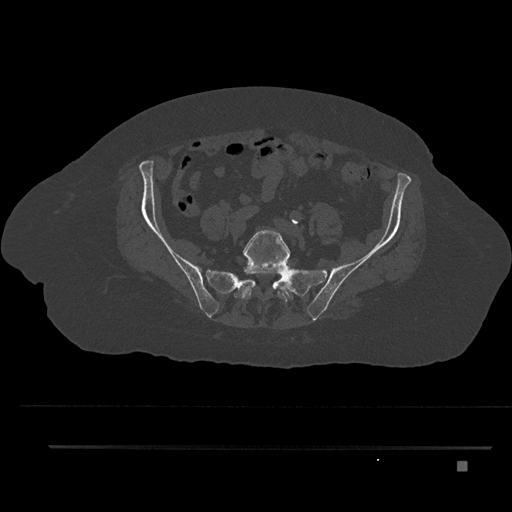
CT including the spine, one axial slice. Position 20 of 797 along the scan axis. Reconstruction kernel Br40s/3. Bone window (W 1800 / L 400 HU). 512 × 512 image matrix, field of view 437 × 437 mm. Patient: female, 76 years. Case-level facts recorded for this patient, not image findings: primary cancer: lung.
Outlined on this slice (semi-automatically segmented with operator editing):
- L5 vertebra: bounding box (x1, y1, x2, y2) in pixels: (241, 229, 290, 302)